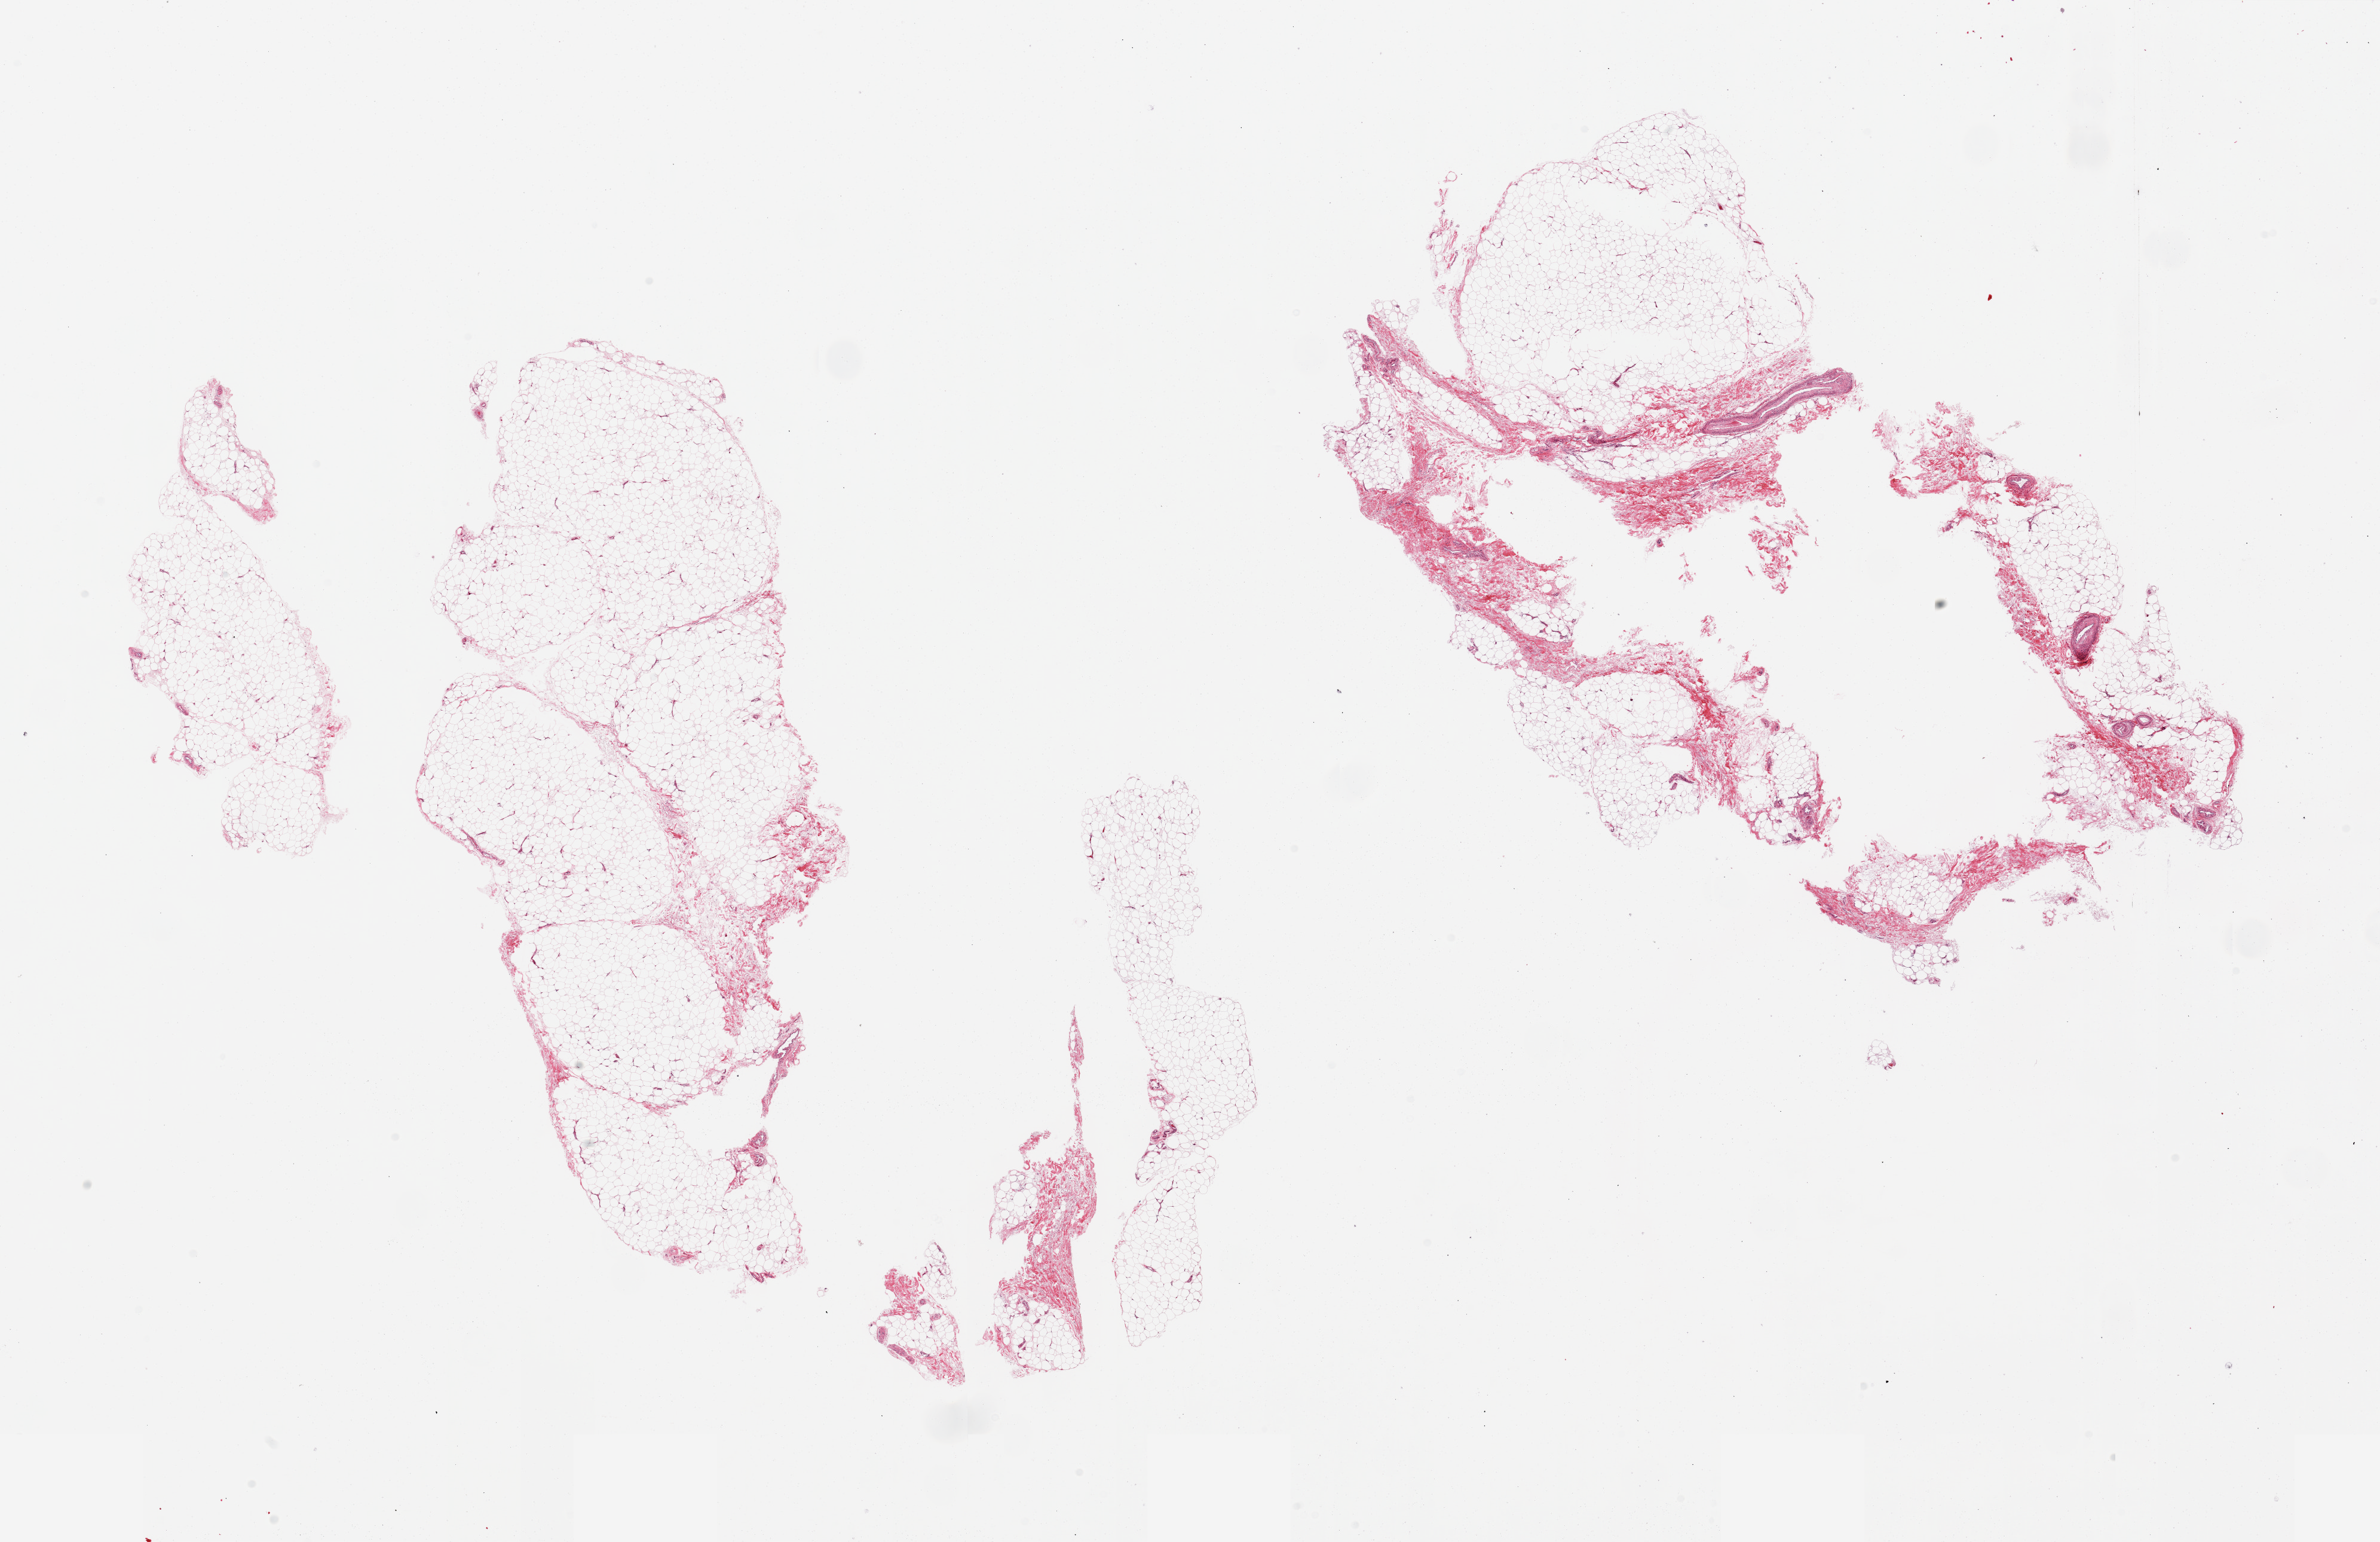
Digitized hematoxylin and eosin (H&E)-stained section — low-resolution overview of the scanned area, about 31.5 x 20.4 mm (from a 20x scan), PAXgene-fixed paraffin-embedded (PFPE) section, section of adipose tissue (target tissue), donor tissue sample. Male donor.
* pathologist's review note for this sample: 2 pieces; several central empty spaces